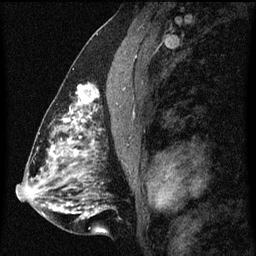
Breast MRI (dynamic contrast-enhanced), one sagittal slice. Slice 30 of 60 in the series (ordered by position). Dynamic contrast-enhanced series, image 2 of 3 at this slice position (ordered by acquisition). 1.5 T. TE 4.2 ms, TR 8 ms. 2 mm slice thickness. 256 × 256 image matrix. Female patient, age 51 years.
Outlined on this slice (semi-automatic segmentation, software-assisted and operator-edited):
- analysis volume of interest (the breast-tissue region the enhancement analysis was run in; not a lesion): bounding box [x1, y1, x2, y2] px = [61, 72, 100, 129]
- tumour enhancement mask (voxels above the 70 % enhancement threshold inside the analysis volume of interest): [61, 84, 100, 129]